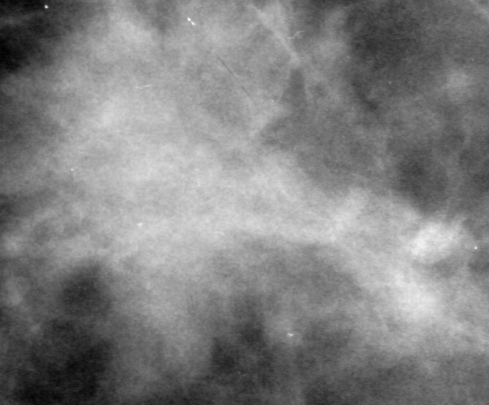
Crop from a digitized film mammogram around one marked abnormality; left breast; CC view.
Marked abnormality: mass, shape irregular, margins spiculated; BI-RADS assessment category 5; pathology result (as recorded, not read from the image): malignant.